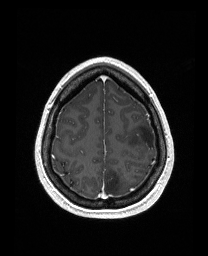
Brain MRI from a brain-tumour surgery series, one axial slice; position 129 of 176 along the scan axis; T1-weighted post-contrast; 1 mm slice thickness; 208 × 256 image matrix, field of view 203 × 250 mm. Case-level facts recorded for this patient, not image findings: histopathology: Astrocytoma; WHO grade: 3; IDH mutation: yes.
Outlined on this slice (outlined manually by an expert reader):
- tumour: bounding box <127,122,156,149> (left, top, right, bottom; pixels)